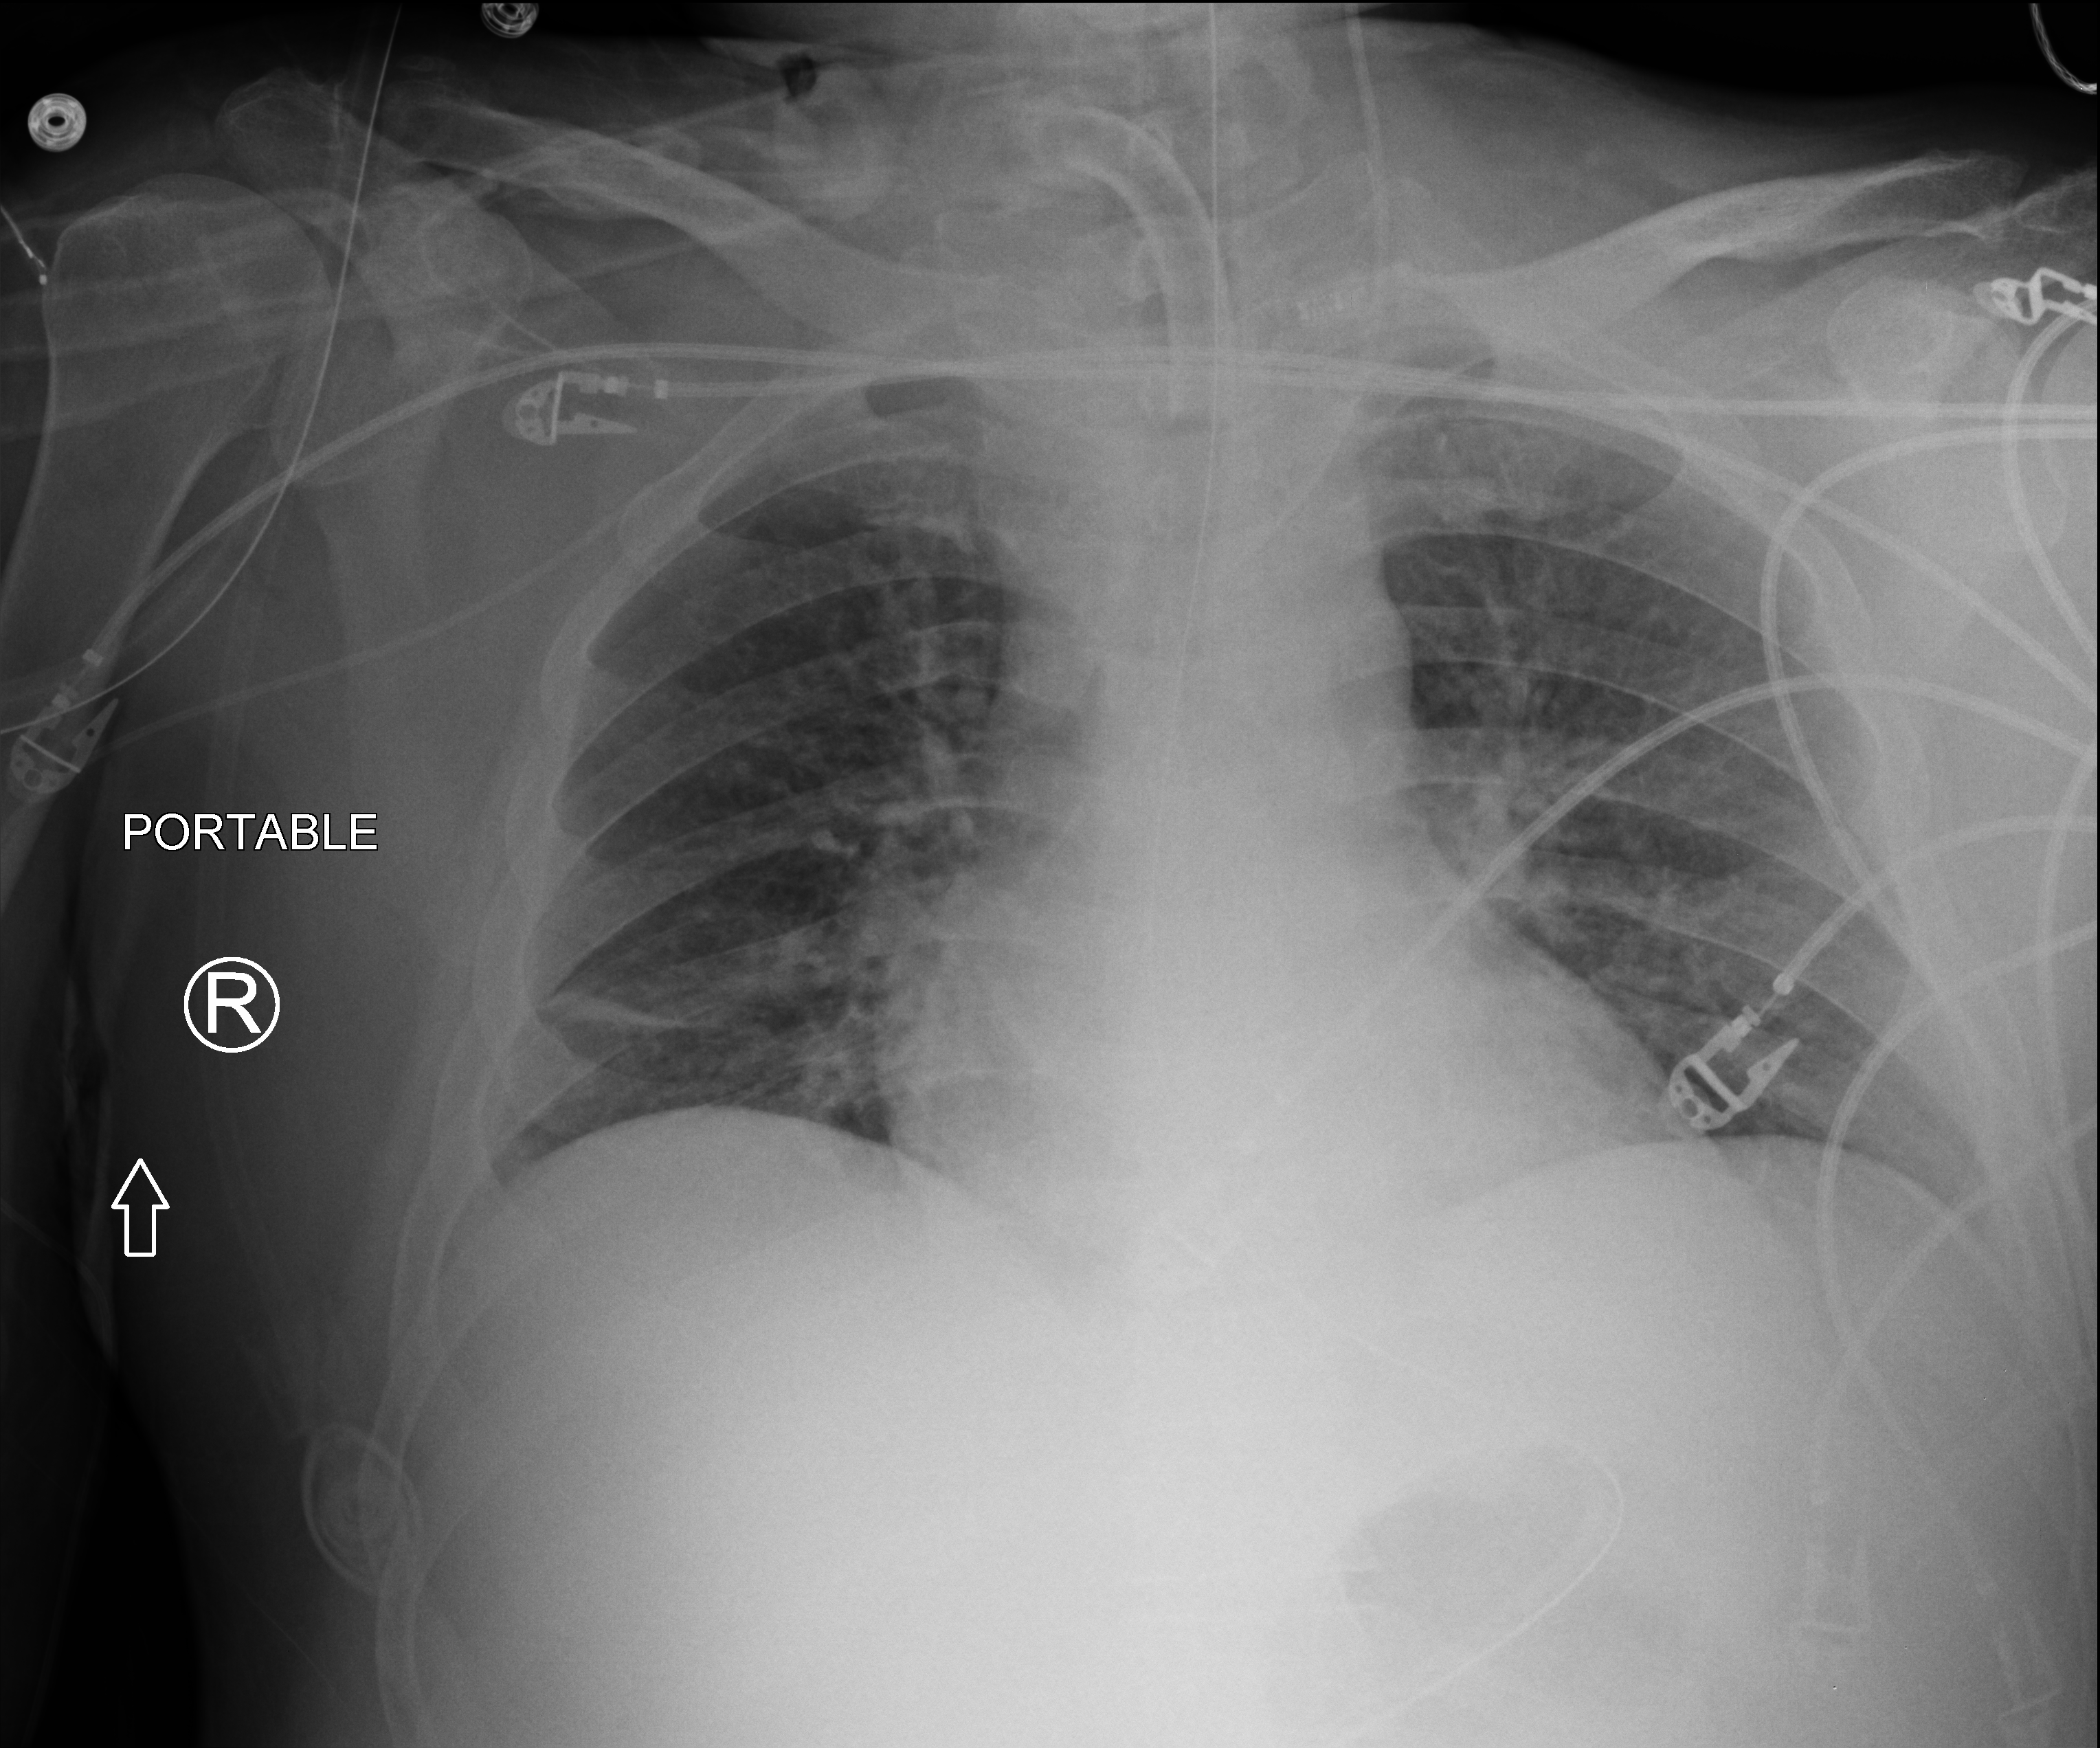
Chest X-ray (portable). Patient hospitalised with COVID-19; male, aged 18–59 years.
From the hospital-stay record, not from the radiograph (when in the stay this image was taken is not recorded):
- mechanically ventilated during this hospital stay: yes